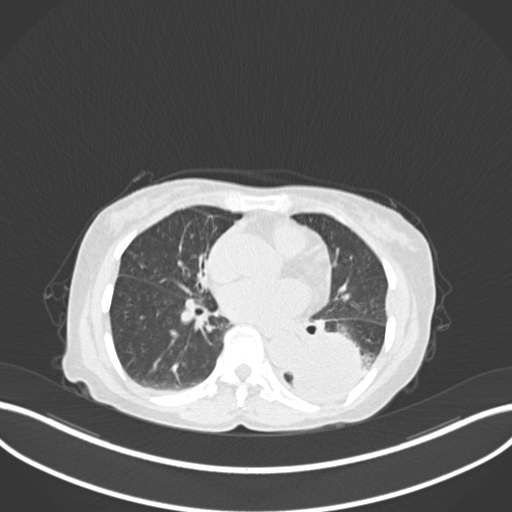
Chest CT, one axial slice. Position 65 of 233 along the scan axis. Lung window (W 1500 / L -600 HU). 1 mm slice thickness. 512 × 512 image matrix, field of view 400 × 400 mm. Female patient, age 78 years. Case-level facts recorded for this patient, not image findings: clinical TNM (as recorded): T3 N0 M1.
Structures marked on this image (bounding box drawn by a radiologist):
- lung tumour (recorded histology: squamous cell carcinoma): bounding box [x1, y1, x2, y2] px = [289, 331, 368, 409]